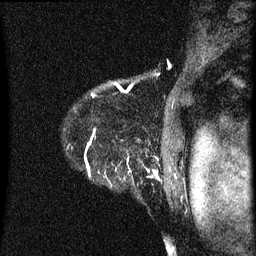
Breast MRI (dynamic contrast-enhanced), one sagittal slice; position 55 of 60 along the scan axis; dynamic contrast-enhanced series, image 2 of 3 at this slice position (ordered by acquisition); 1.5 T; TE 4.2 ms, TR 8 ms; 256 × 256 image matrix. Female patient, age 54 years.
Outlined on this slice (semi-automatically segmented with operator editing):
- analysis volume of interest (the breast-tissue region the enhancement analysis was run in; not a lesion): bounding box (x1, y1, x2, y2) in pixels: (66, 138, 164, 199)
- tumour enhancement mask (voxels above the 70 % enhancement threshold inside the analysis volume of interest): (85, 138, 159, 179)